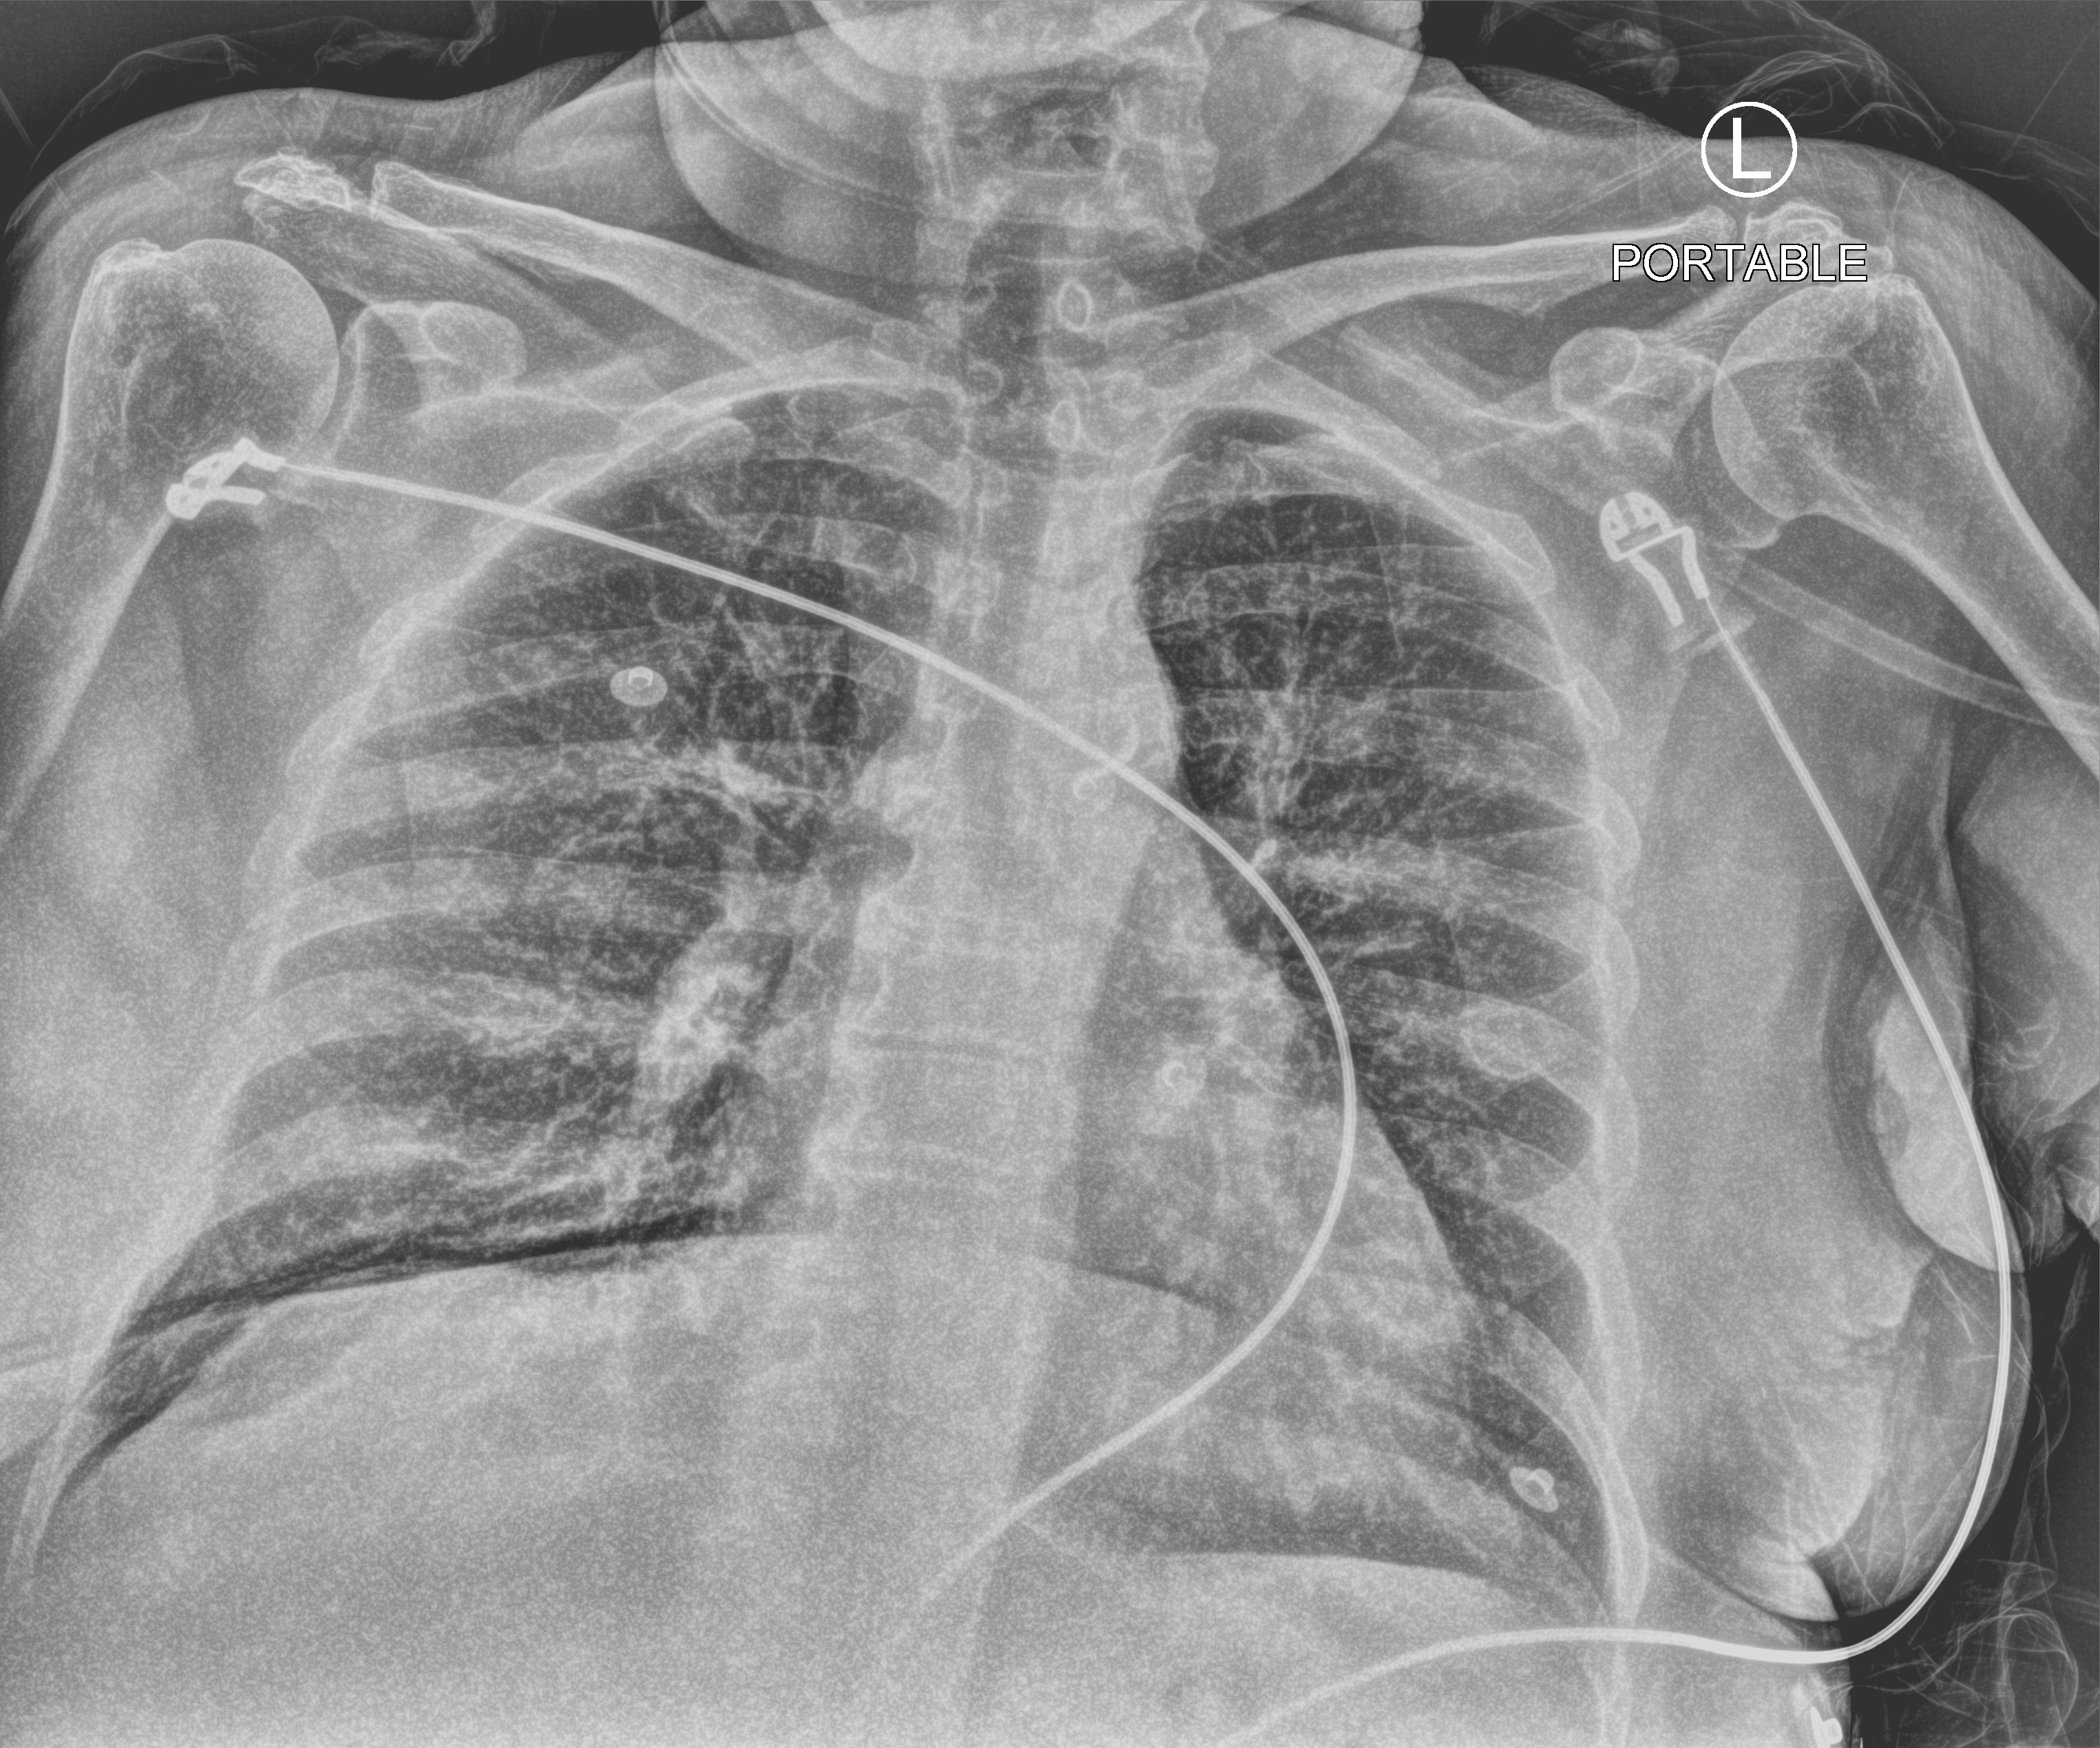
Portable chest radiograph, anteroposterior (AP) projection. Female patient hospitalised with COVID-19, age 75–90 years.
Admission-level facts for this patient (not findings on this image; timing relative to this image not recorded): length of hospital stay: 6 days.